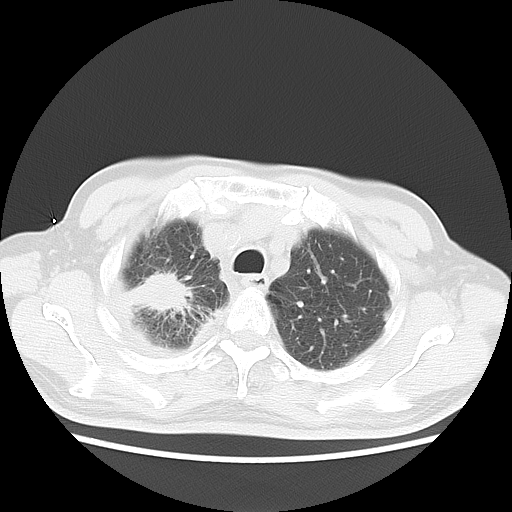
Chest CT, one axial slice; reconstruction kernel LUNG; 120 kVp; lung window (W 1500 / L -600 HU); 512 × 512 image matrix, field of view 350 × 350 mm. Patient: male, 75 years. From the clinical record (not read from this slice): clinical TNM (as recorded): T1c N1 M1.
Structures marked on this image (rectangle marked by the reading radiologist):
- lung tumour (recorded histology: adenocarcinoma): bounding box [x1, y1, x2, y2] px = [121, 265, 190, 324]